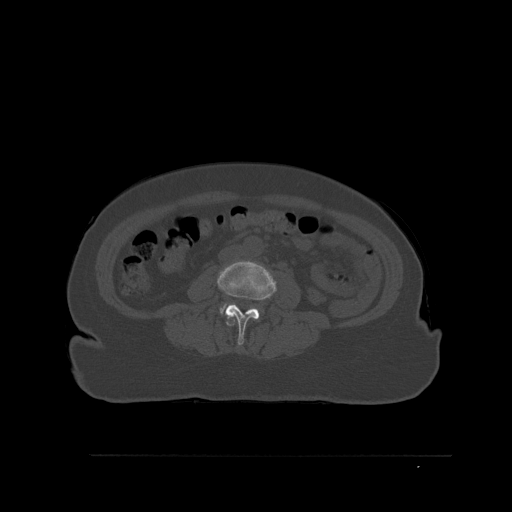
CT including the spine, one axial slice. Slice 222 of 527 in the series (ordered by position). Bone window (W 1800 / L 400 HU). 1.5 mm slice thickness. 512 × 512 image matrix, field of view 470 × 470 mm. Patient: female, 73 years. From the clinical record (not read from this slice): primary cancer: breast; vertebrae with lytic lesions (as recorded): L2.
Outlined on this slice (semi-automatically segmented with operator editing):
- L2 vertebra: bounding box [x1, y1, x2, y2] px = [227, 319, 235, 326]
- L3 vertebra: [217, 260, 277, 345]
- L4 vertebra: [220, 304, 260, 313]